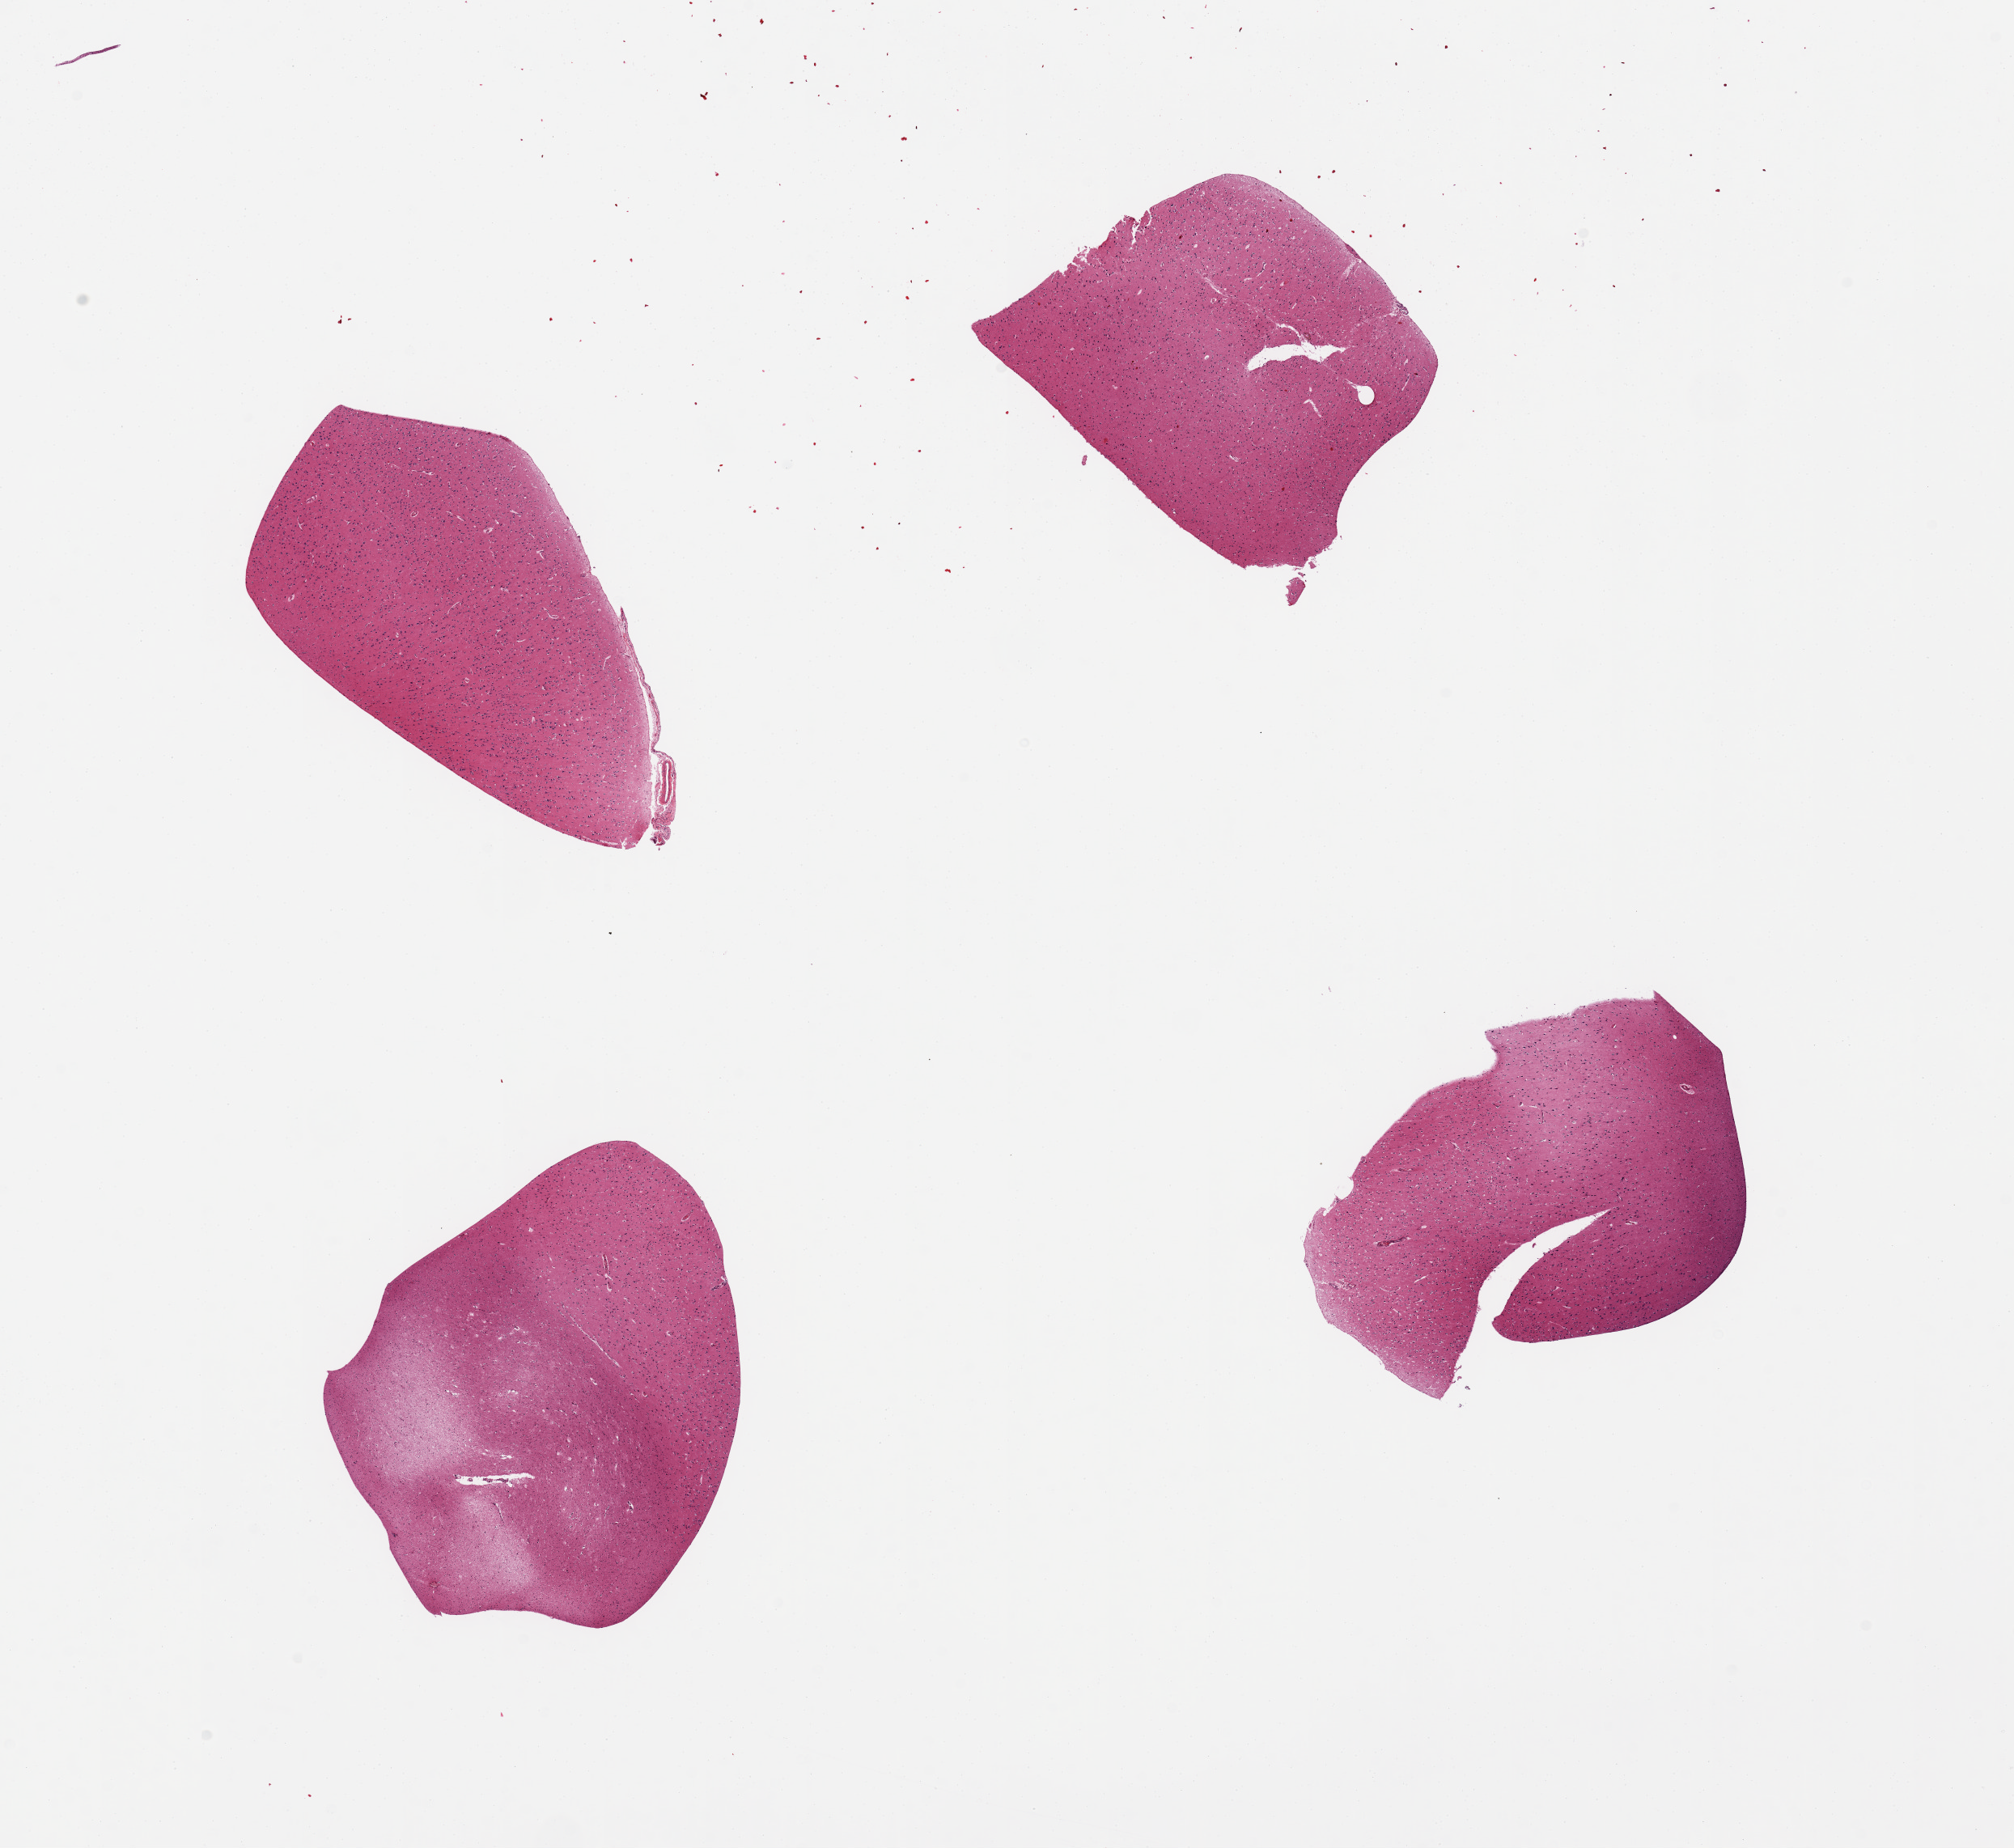
Haematoxylin and eosin whole-slide image — whole scanned area (about 19.7 x 18.1 mm, slide scanned at 20x) shown as a low-resolution overview, PAXgene-fixed, paraffin-embedded tissue, sampled site (target tissue): cerebral cortex, tissue donor sample. Male donor.
- review note (as recorded): 4 pieces